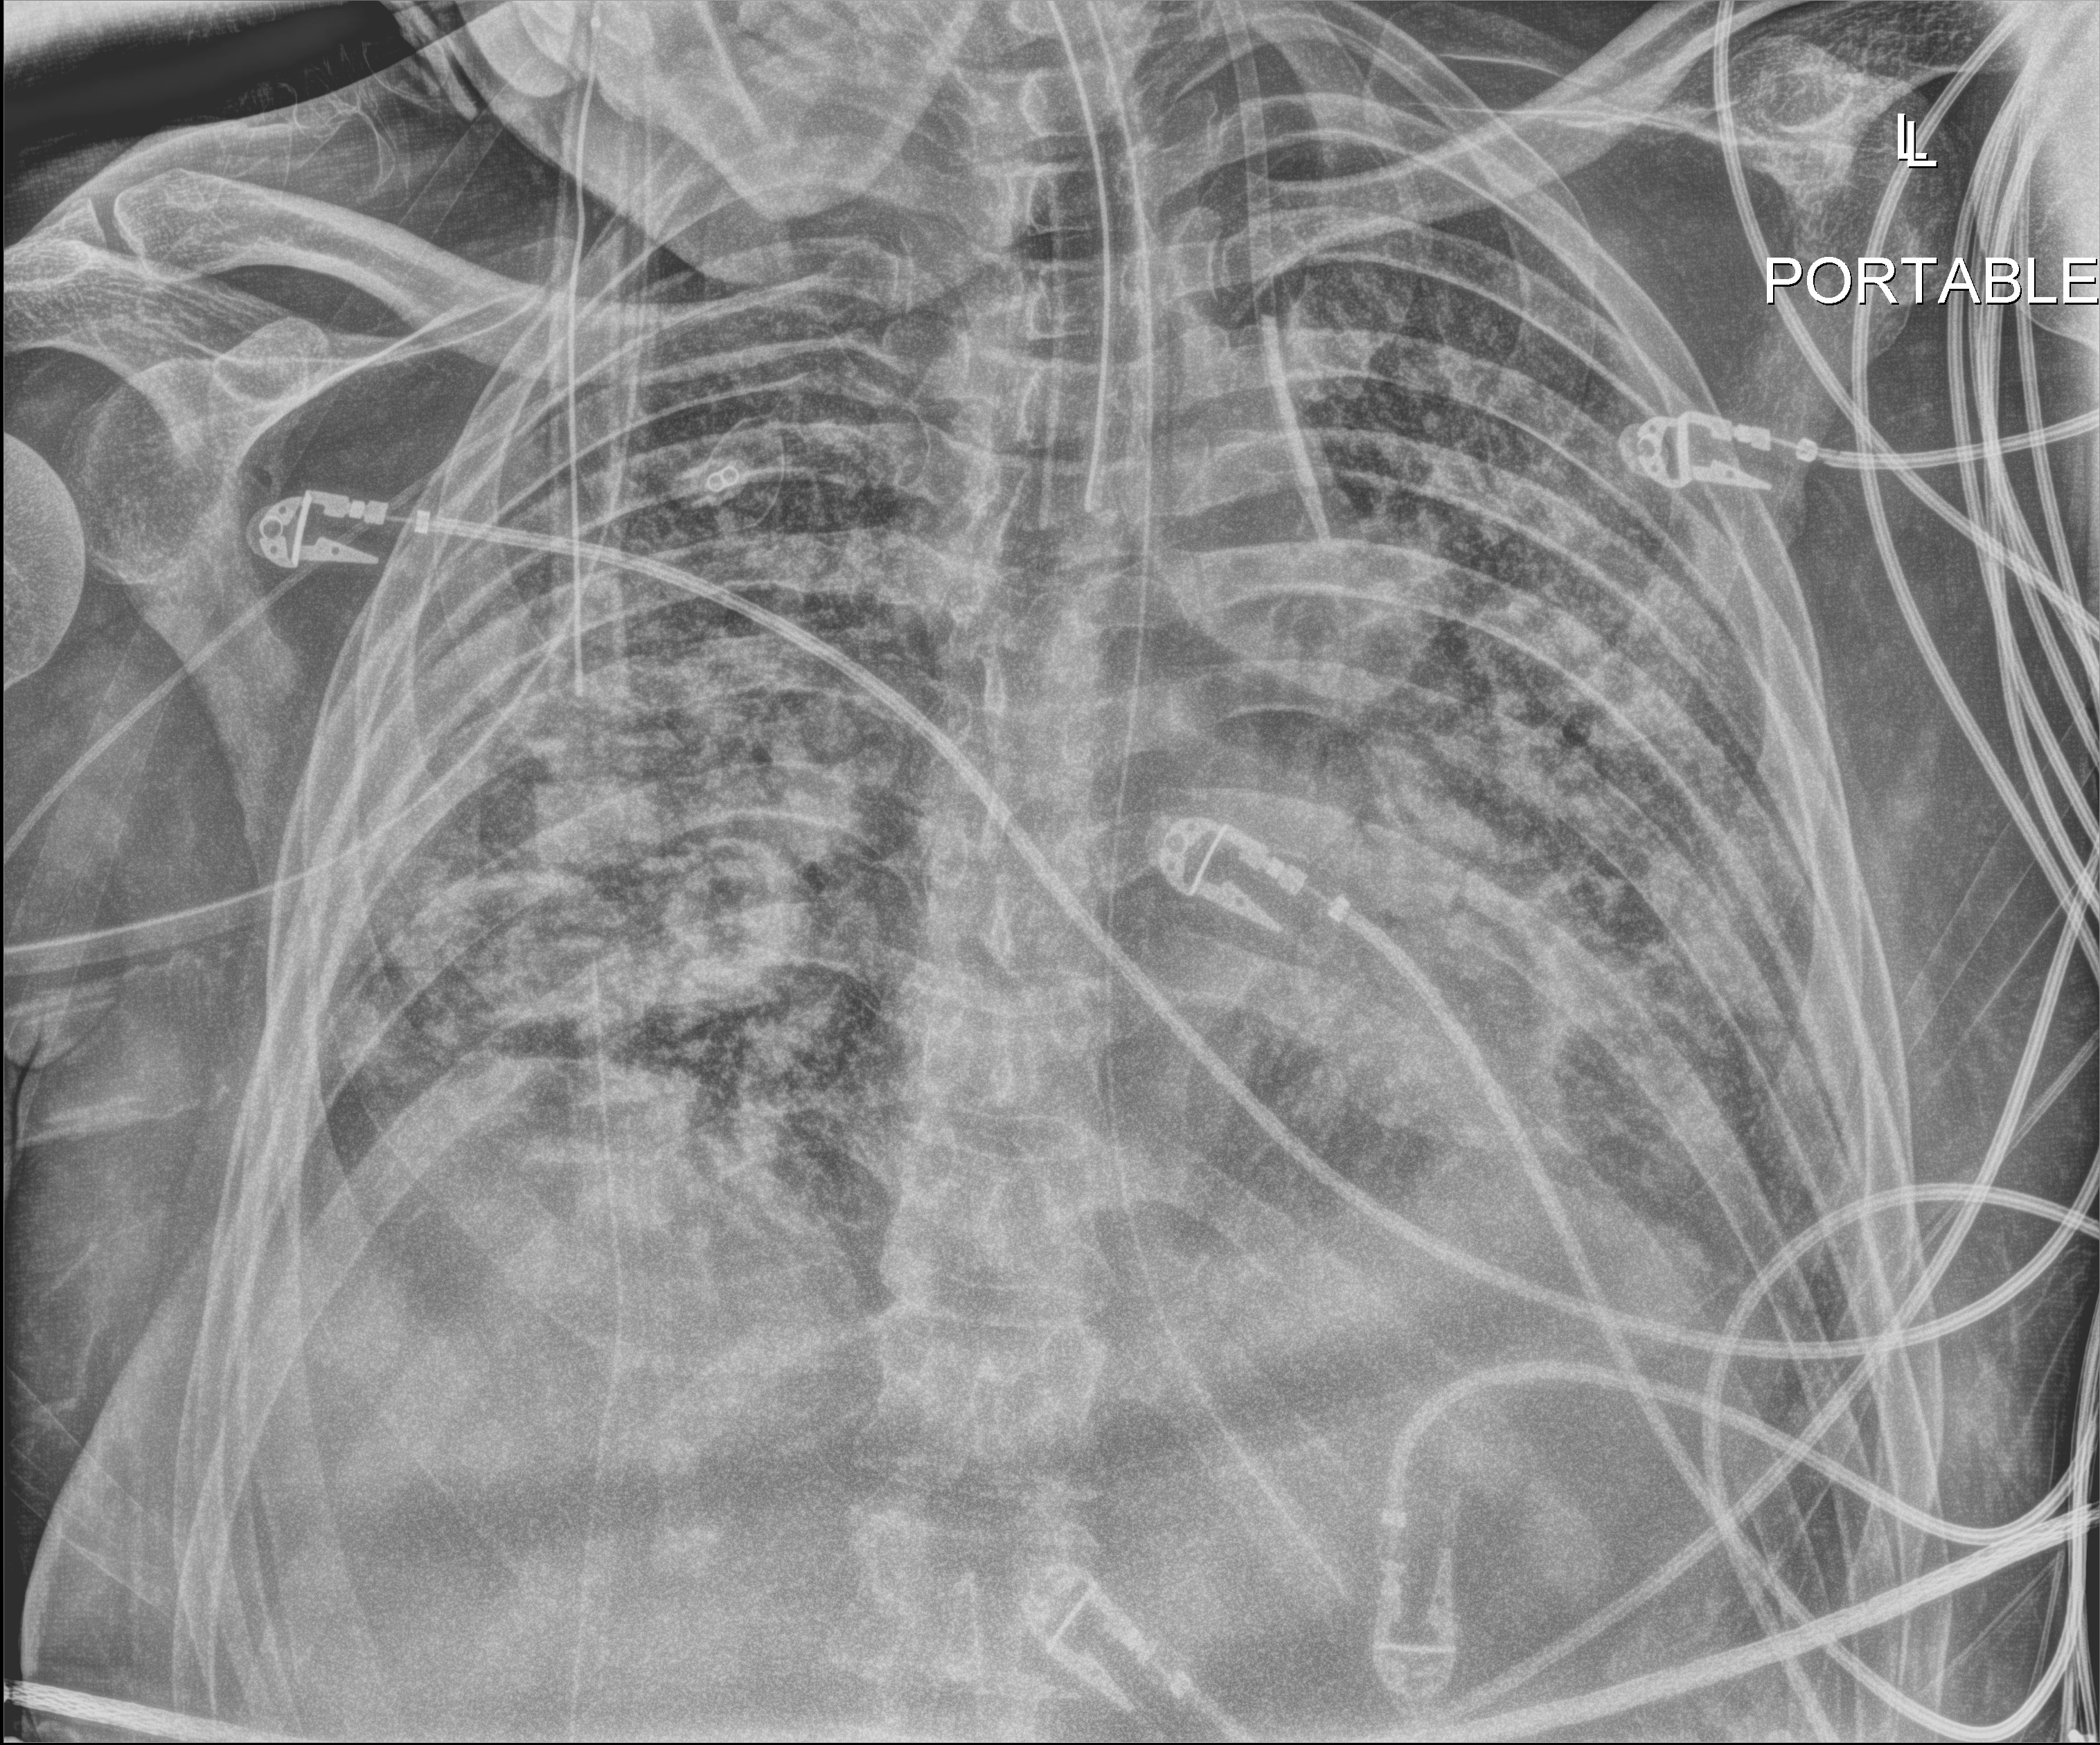
Chest radiograph; anteroposterior (AP) projection. Male patient hospitalised with COVID-19, age 18–59 years.
Hospital-stay facts (about this admission, not read from this image; timing relative to this image not recorded): admitted to intensive care during this hospital stay: yes; diabetes (admission record): no; length of hospital stay: 75 days.